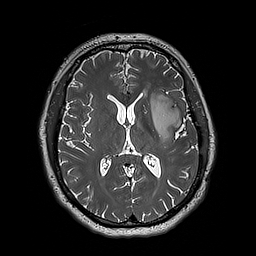
Brain MRI from a brain-tumour surgery series, one axial slice; slice 98 of 192 in the series (ordered by position); 1 mm slice thickness; 256 × 256 image matrix, field of view 250 × 250 mm. From the clinical record (not read from this slice): histopathology: Astrocytoma; WHO grade: 3; IDH mutation: yes; tumour location: Left Insular.
Annotated regions visible in this slice (expert manual segmentation):
- tumour: bounding box (x1, y1, x2, y2) in pixels: (150, 94, 184, 143)